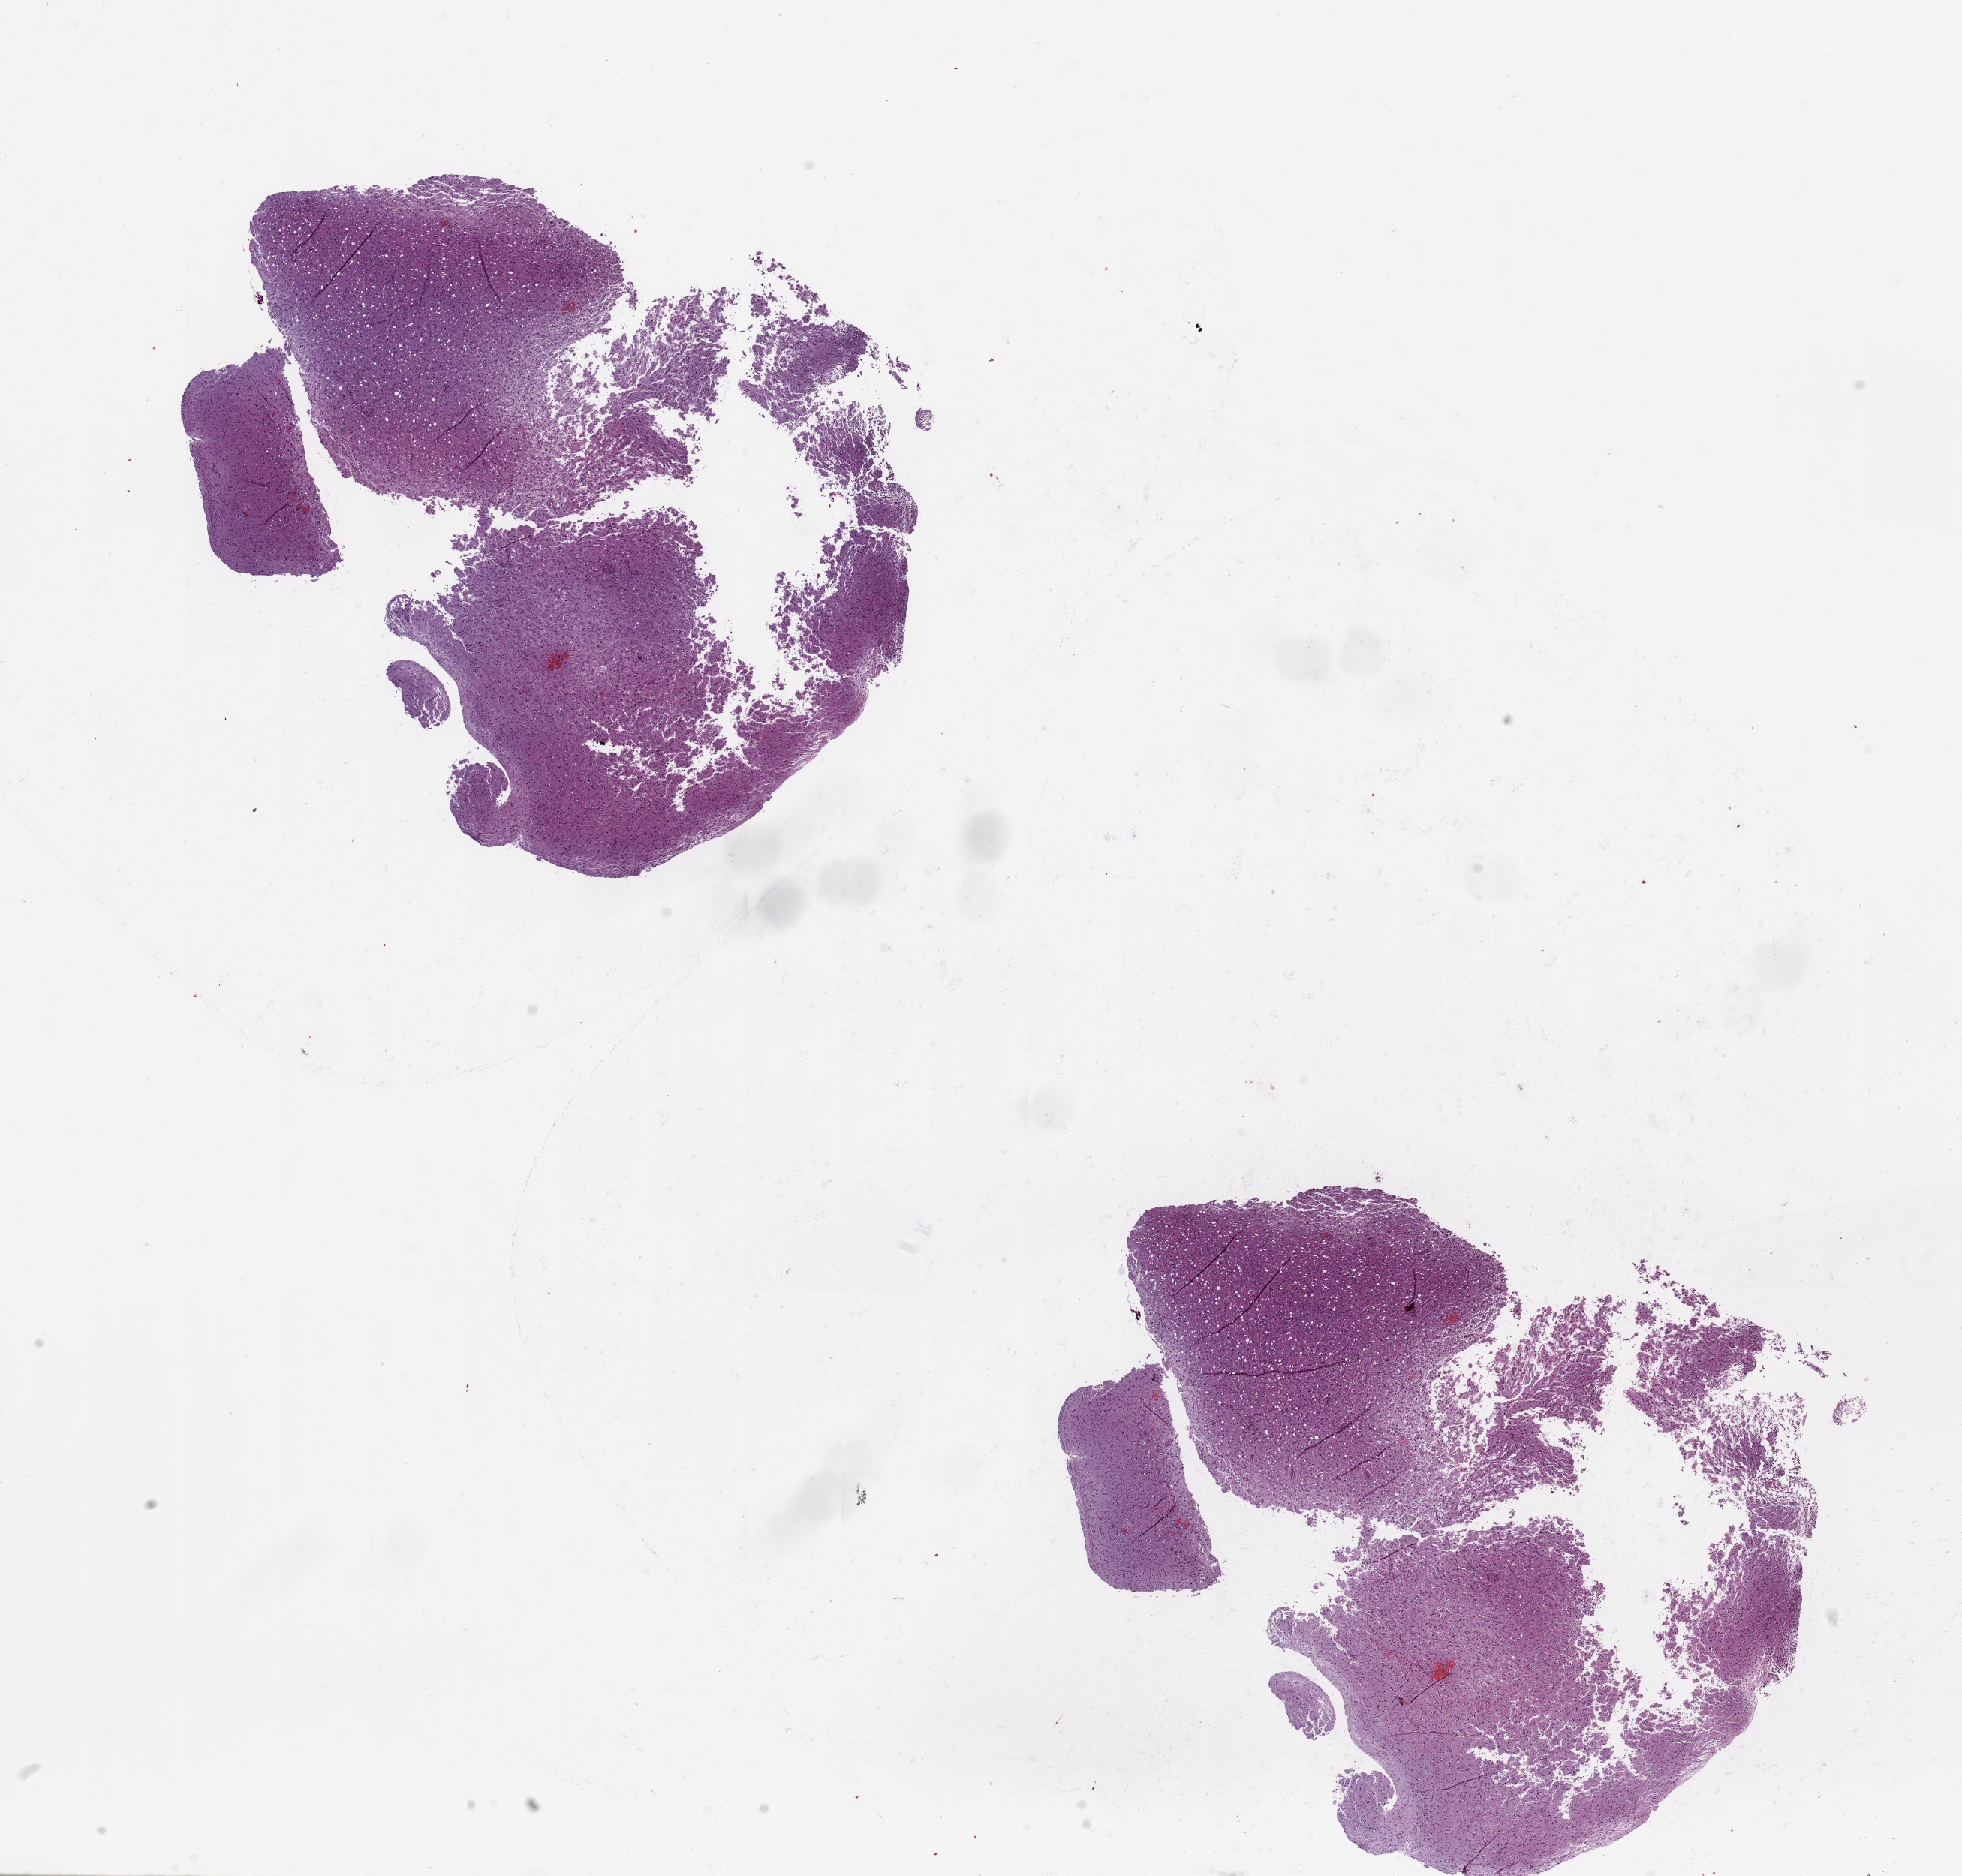
H&E whole-slide image, whole scanned area (about 20.7 x 19.8 mm) shown as a low-resolution overview. Tumour tissue sample, sampled site: frontal lobe. Patient: male, age 53 years. Slide review estimates, as recorded: tumour nuclei 75%, necrosis 5%.
Diagnosis: Glioblastoma.